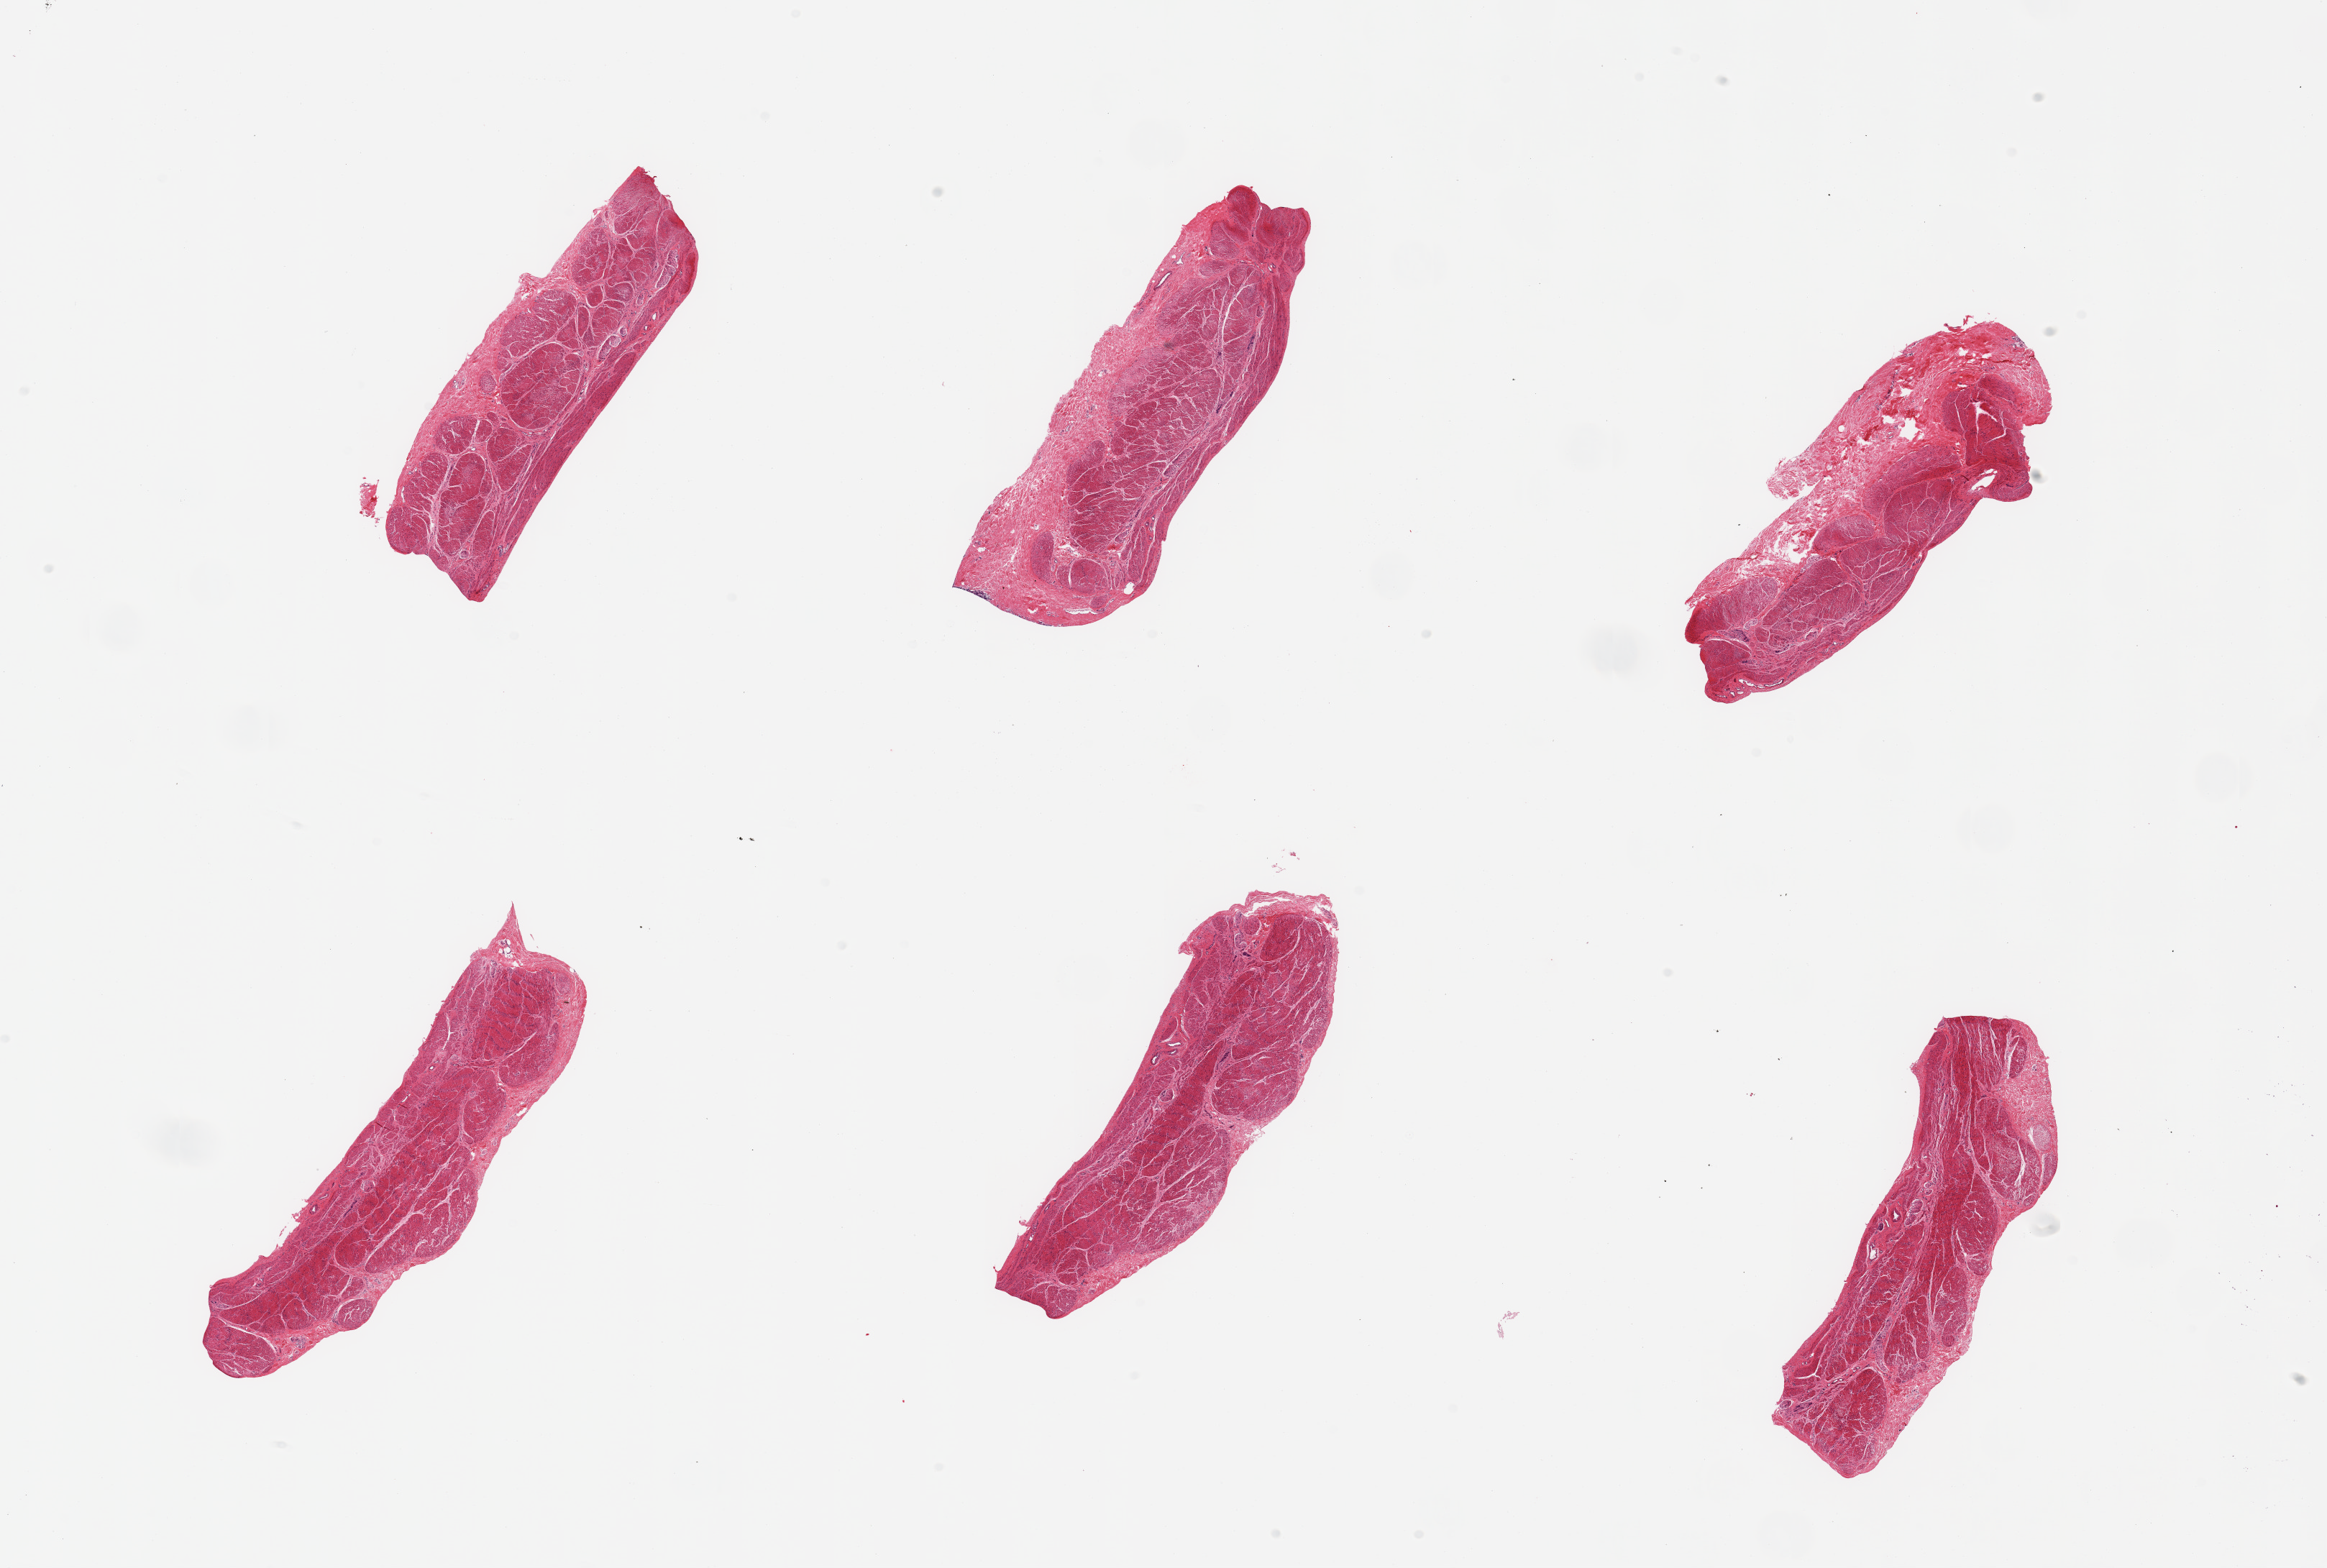
Whole-slide image, hematoxylin and eosin (H&E) stain — a low-resolution overview of the entire scanned area, about 25.6 x 17.3 mm. PAXgene-fixed paraffin-embedded (PFPE) section. Target tissue: stomach. Tissue donor sample.
- review note (as recorded): 6 pieces, muscularis only; no target mucosa present